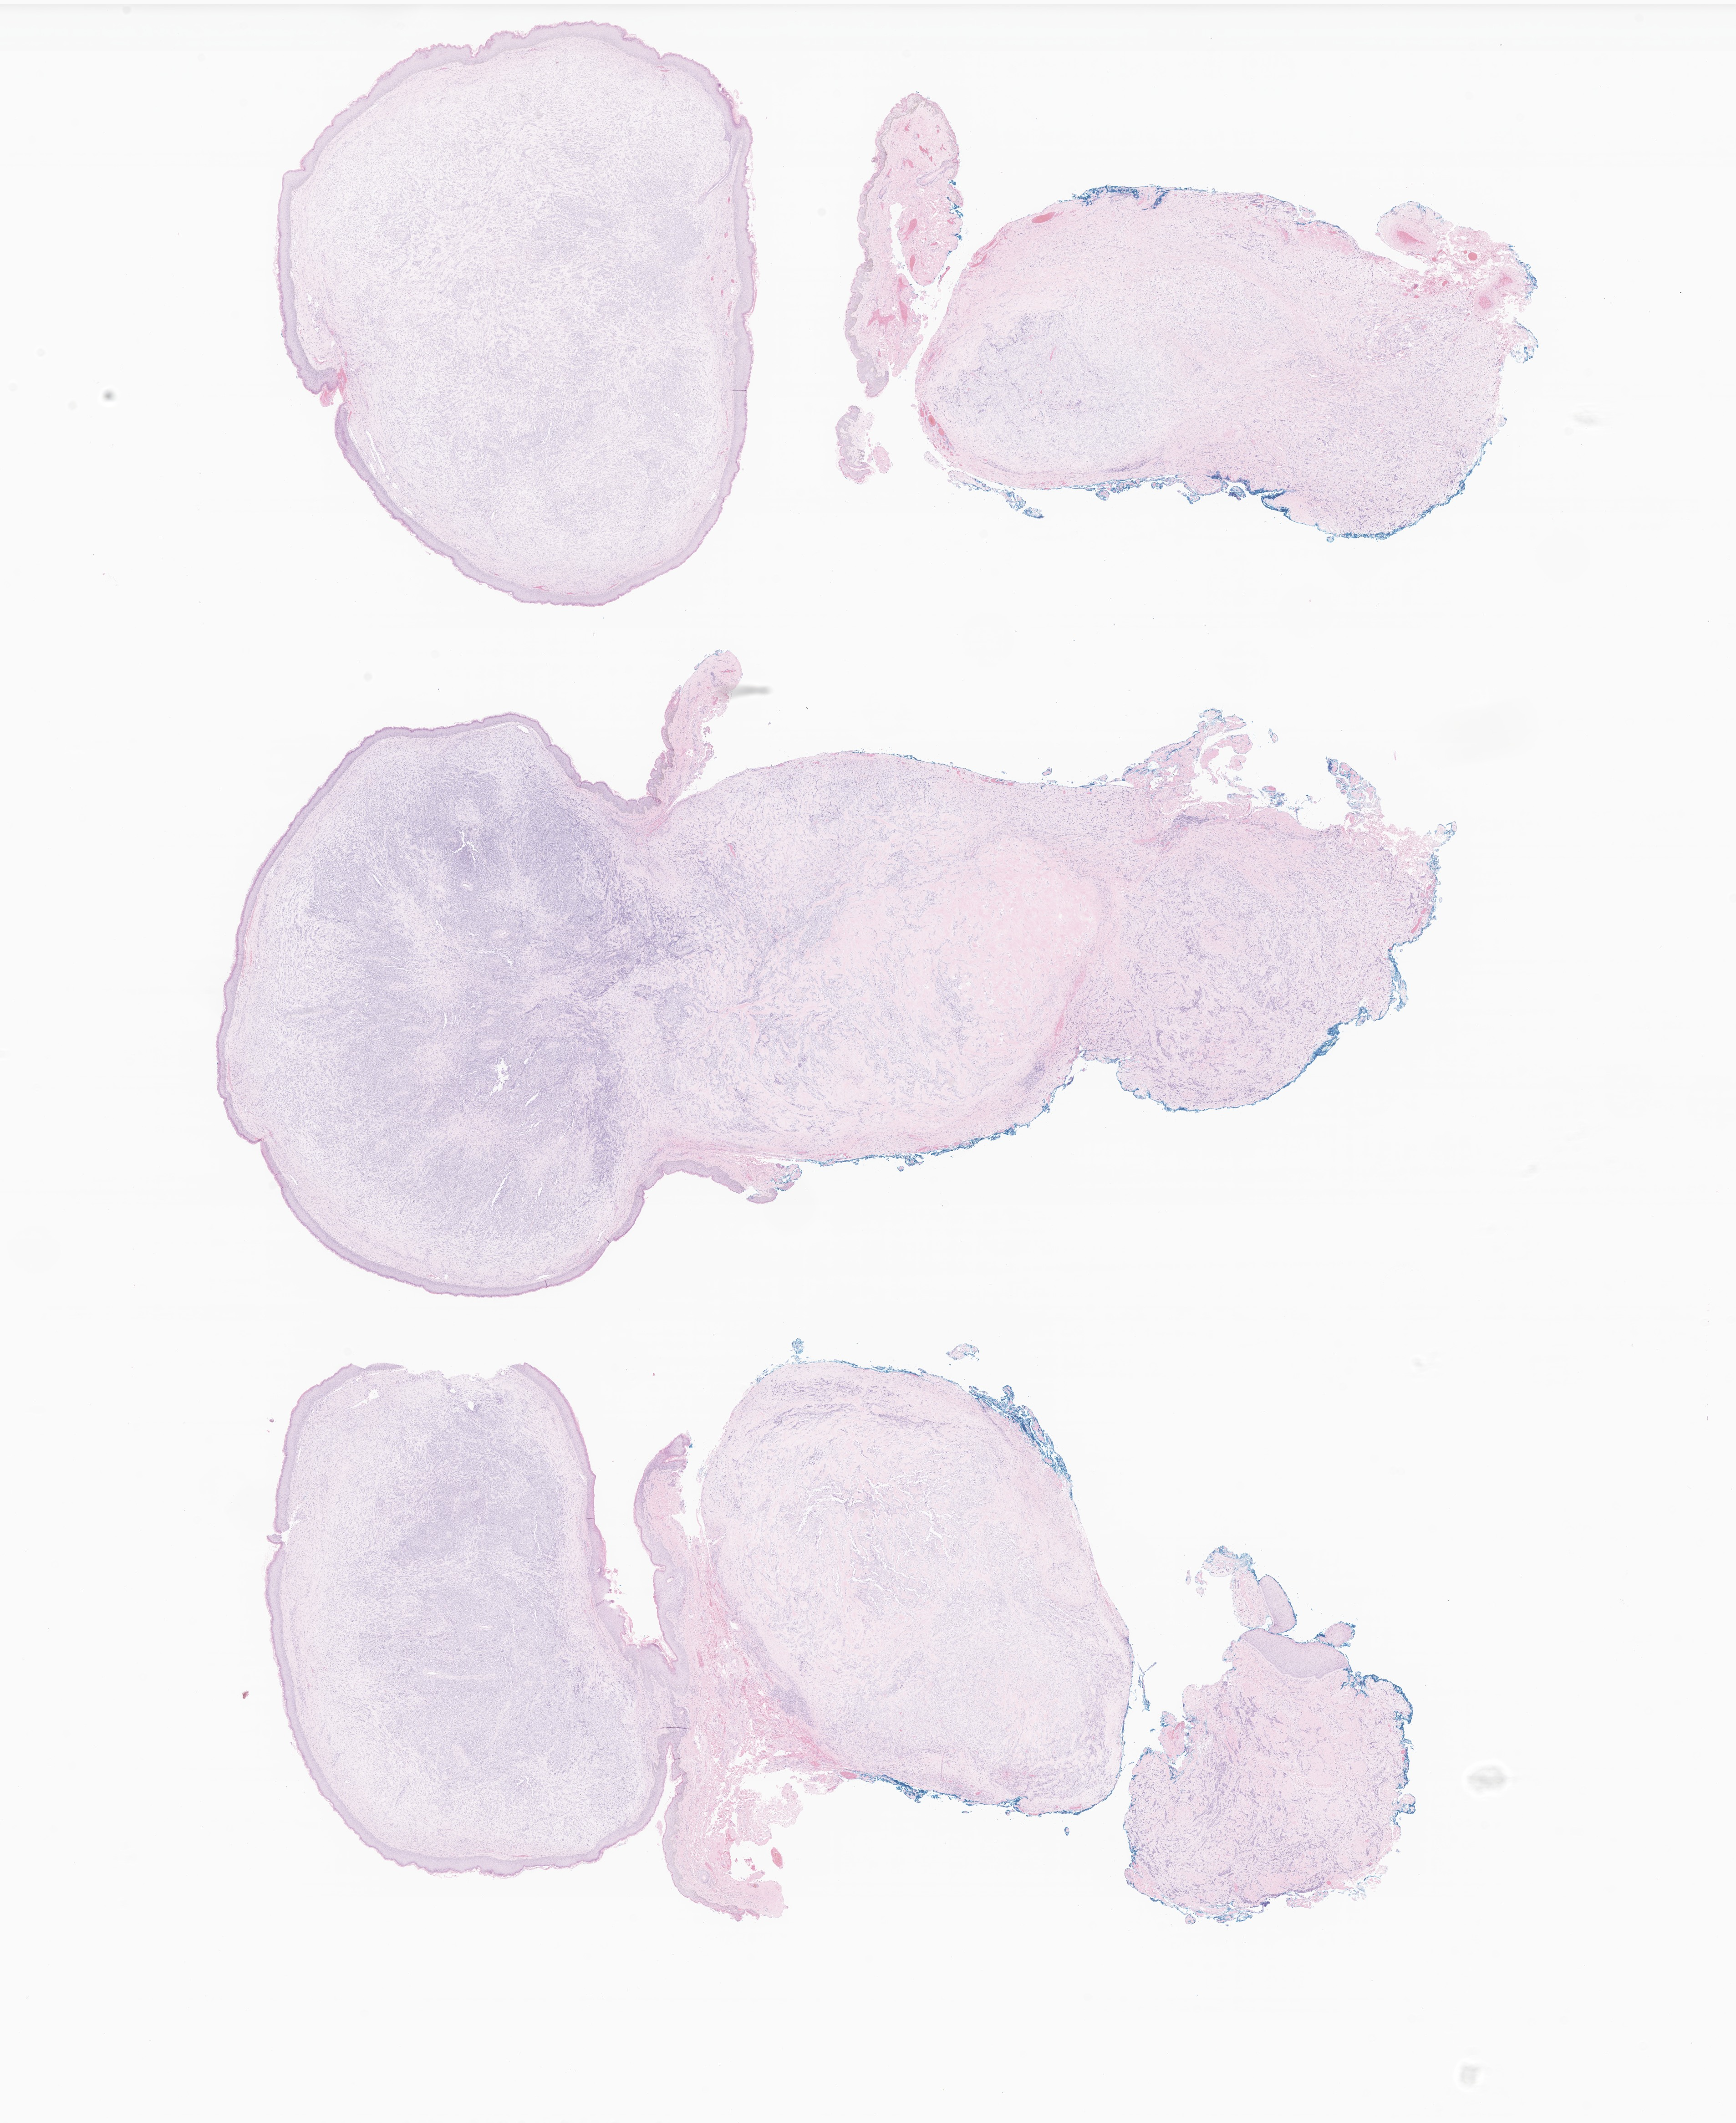
Digitized H&E-stained section of tumor tissue from the eyelid — whole scanned area (about 16.1 x 19.7 mm) shown as a low-resolution overview. Formalin-fixed, paraffin-embedded (FFPE) tissue. Patient: male, age 75 months.
Recorded diagnosis: Rhabdomyosarcoma, NOS.